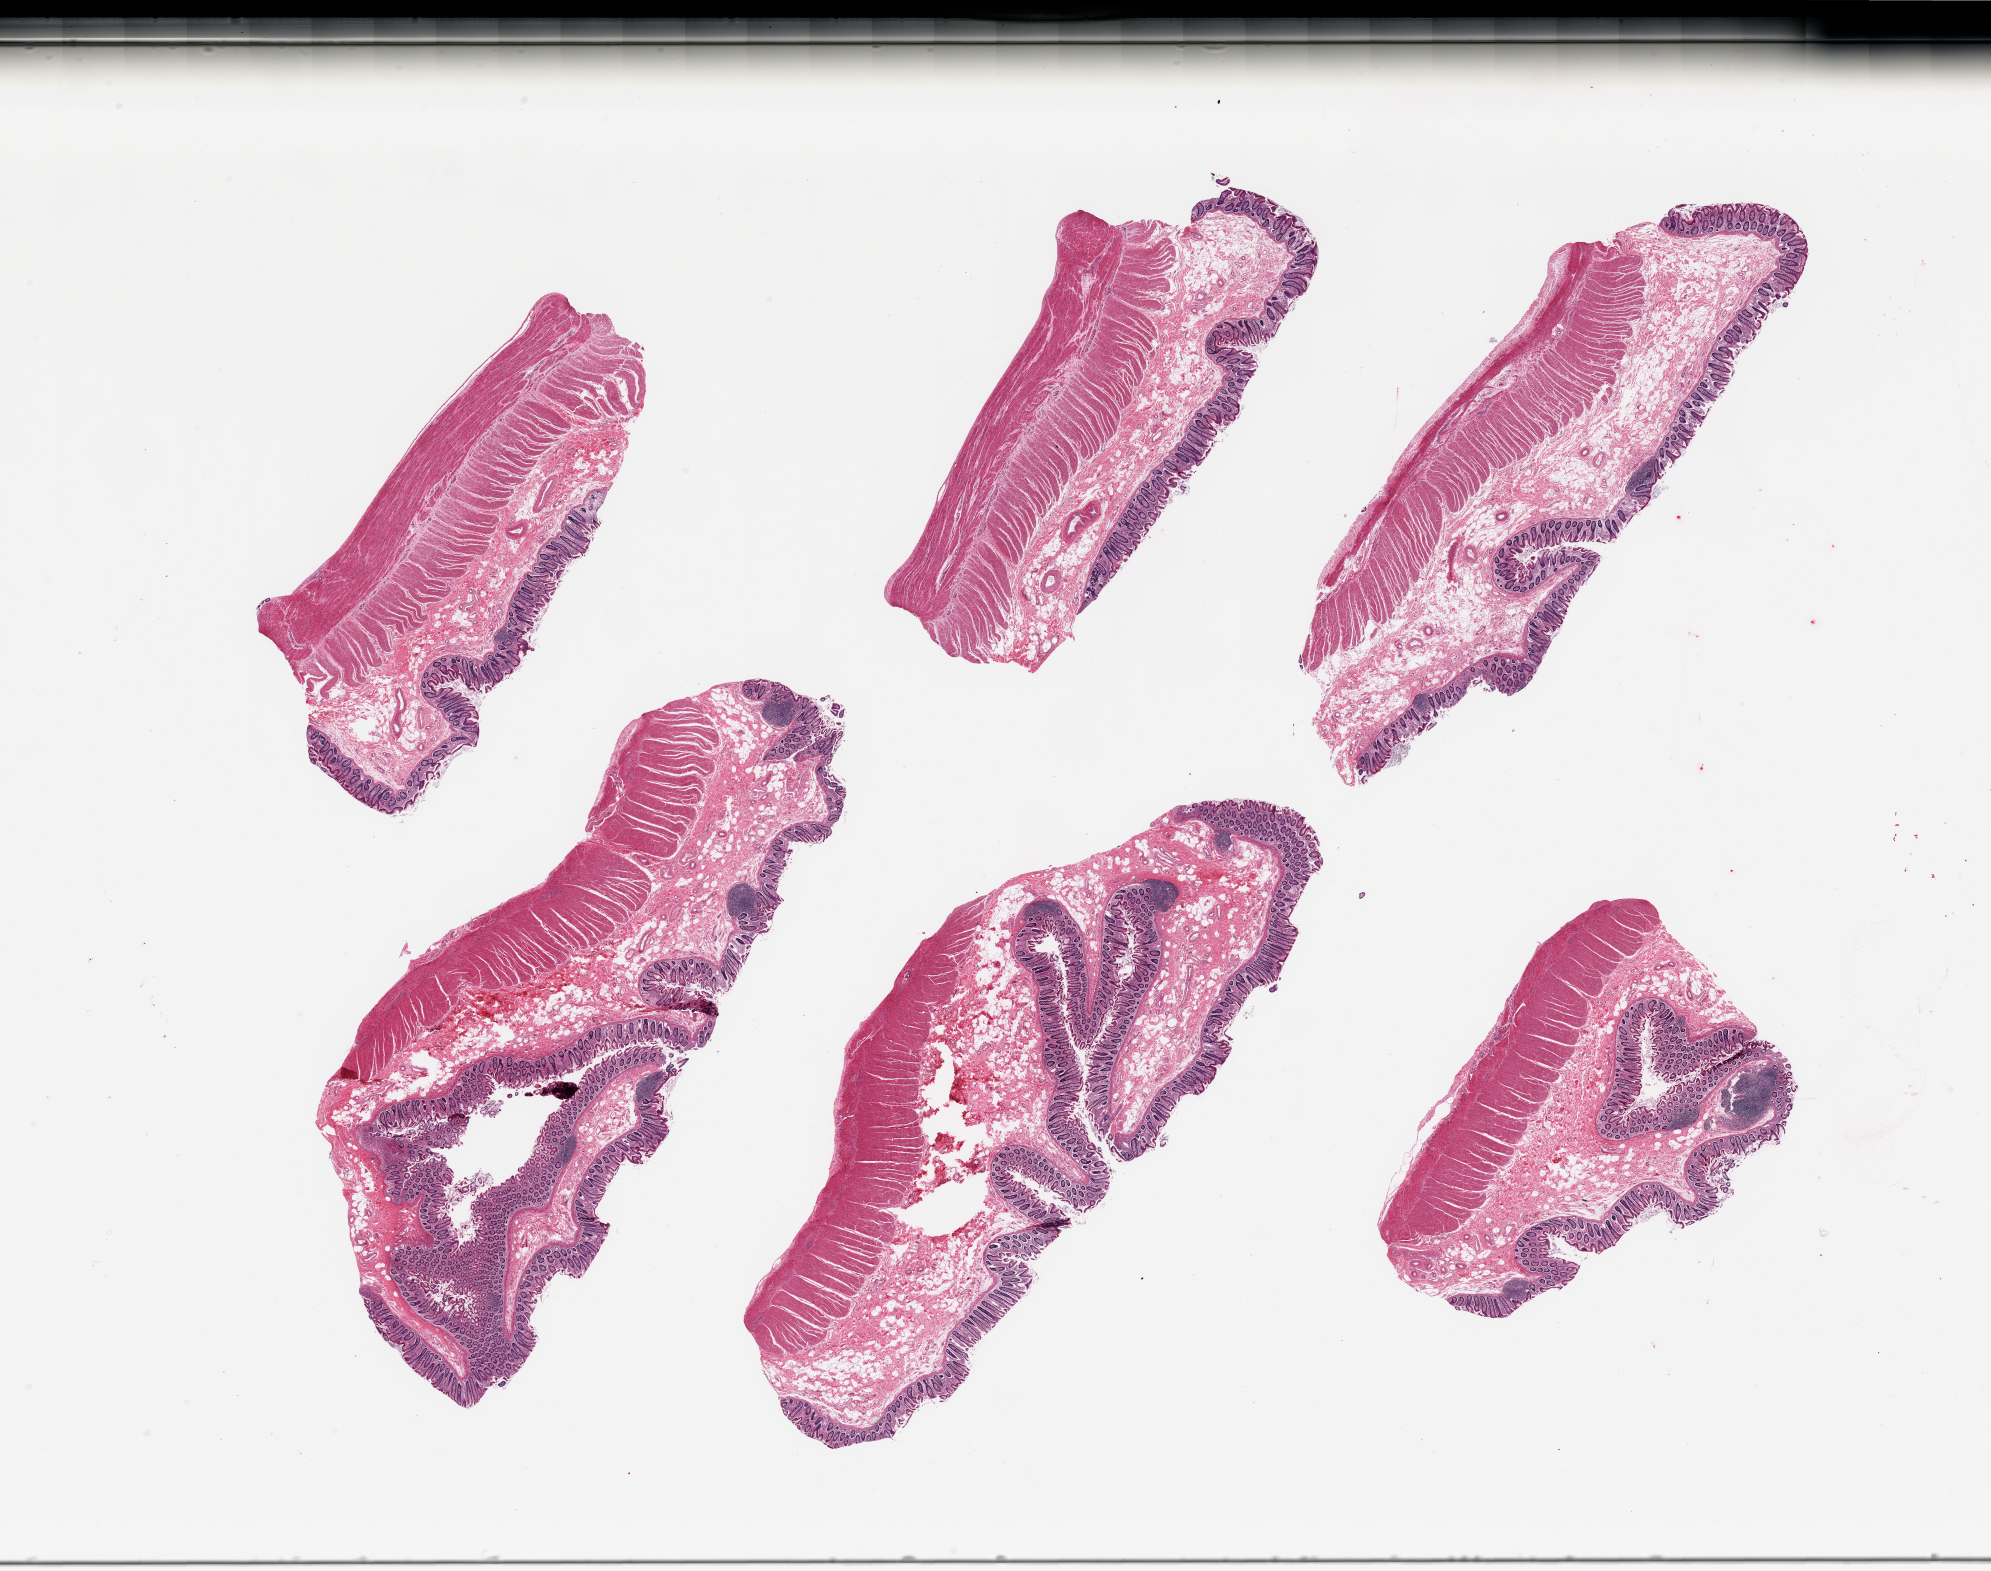
Whole-slide image, H&E stain — shown as a low-resolution overview of the whole scanned area (about 31.5 x 24.9 mm, acquisition: 20x scan). PAXgene-fixed, paraffin-embedded tissue. Target tissue: transverse colon. Tissue donor sample. Donor sex: male.
Reviewer comment on this tissue sample: 6 pieces; well preserved colonic mucosa and muscularis and lymphoid aggregates.